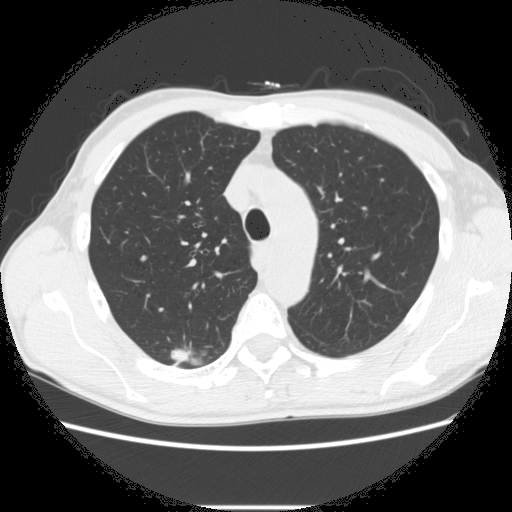
Axial slice from a low-dose chest CT screening exam; second screening round (one year after baseline); lung window (W 1500 / L -600 HU); 2.5 mm slice thickness; standard (soft-tissue) reconstruction kernel (STANDARD); 512 × 512 image matrix, field of view 360 × 360 mm. Male participant, aged 66 years at enrolment.
- Lesion marked by an expert reader, box from (x=161, y=337) to (x=222, y=373) px.
- The screening reader recorded 5 non-calcified nodules or masses ≥4 mm on this exam (right lower lobe, right upper lobe, right upper lobe, right upper lobe, left lower lobe); which of them this box marks is not recorded.
- Official screen result: positive, change unspecified: nodule(s) >= 4 mm or enlarging nodule(s), mass(es), or other non-specific abnormalities suspicious for lung cancer.
- Participant outcome: lung cancer diagnosed 75 days after this screen — adenocarcinoma, NOS, right upper lobe, undifferentiated (G4), stage IA (AJCC 6th edition), 20 mm at pathology.